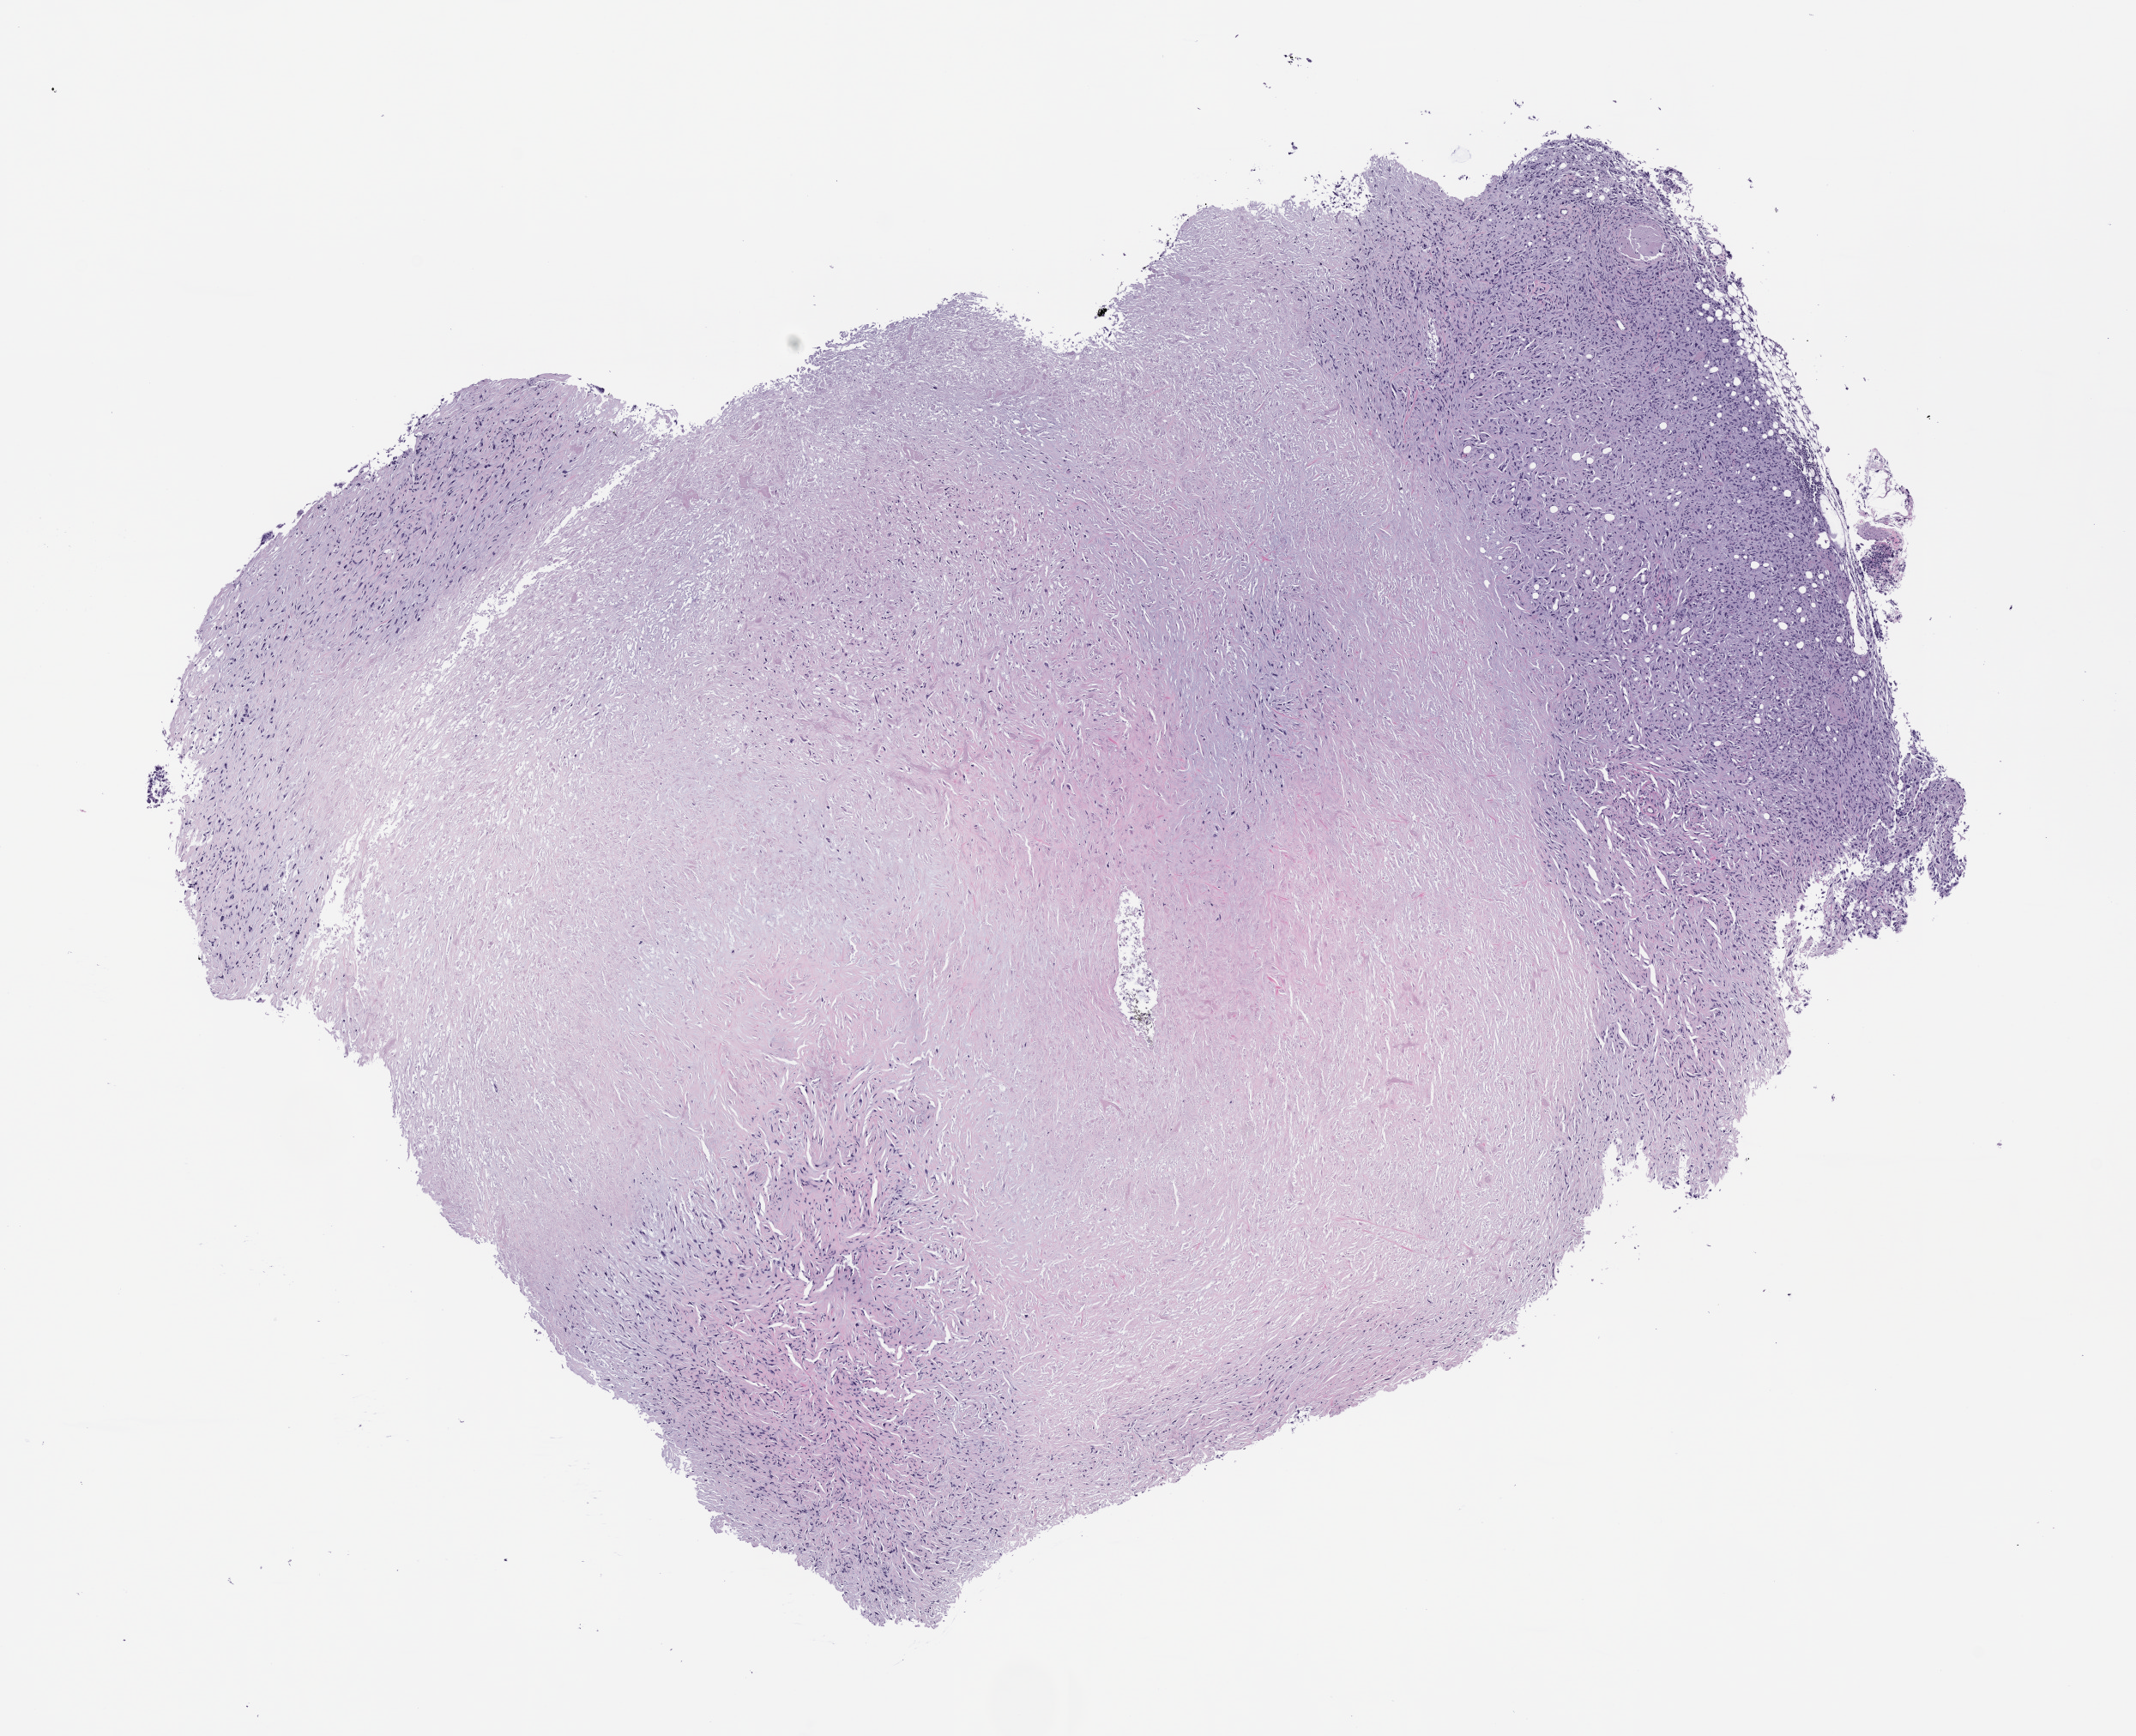
Whole-slide image, hematoxylin and eosin (H&E): patient-derived xenograft (human tumor grown in a mouse), a low-resolution overview of the entire scanned area, about 10.0 x 8.1 mm. Formalin-fixed, paraffin-embedded (FFPE) tissue. Originating tumor site category: musculoskeletal.
• originating patient diagnosis: Spindle Cell Sarcoma